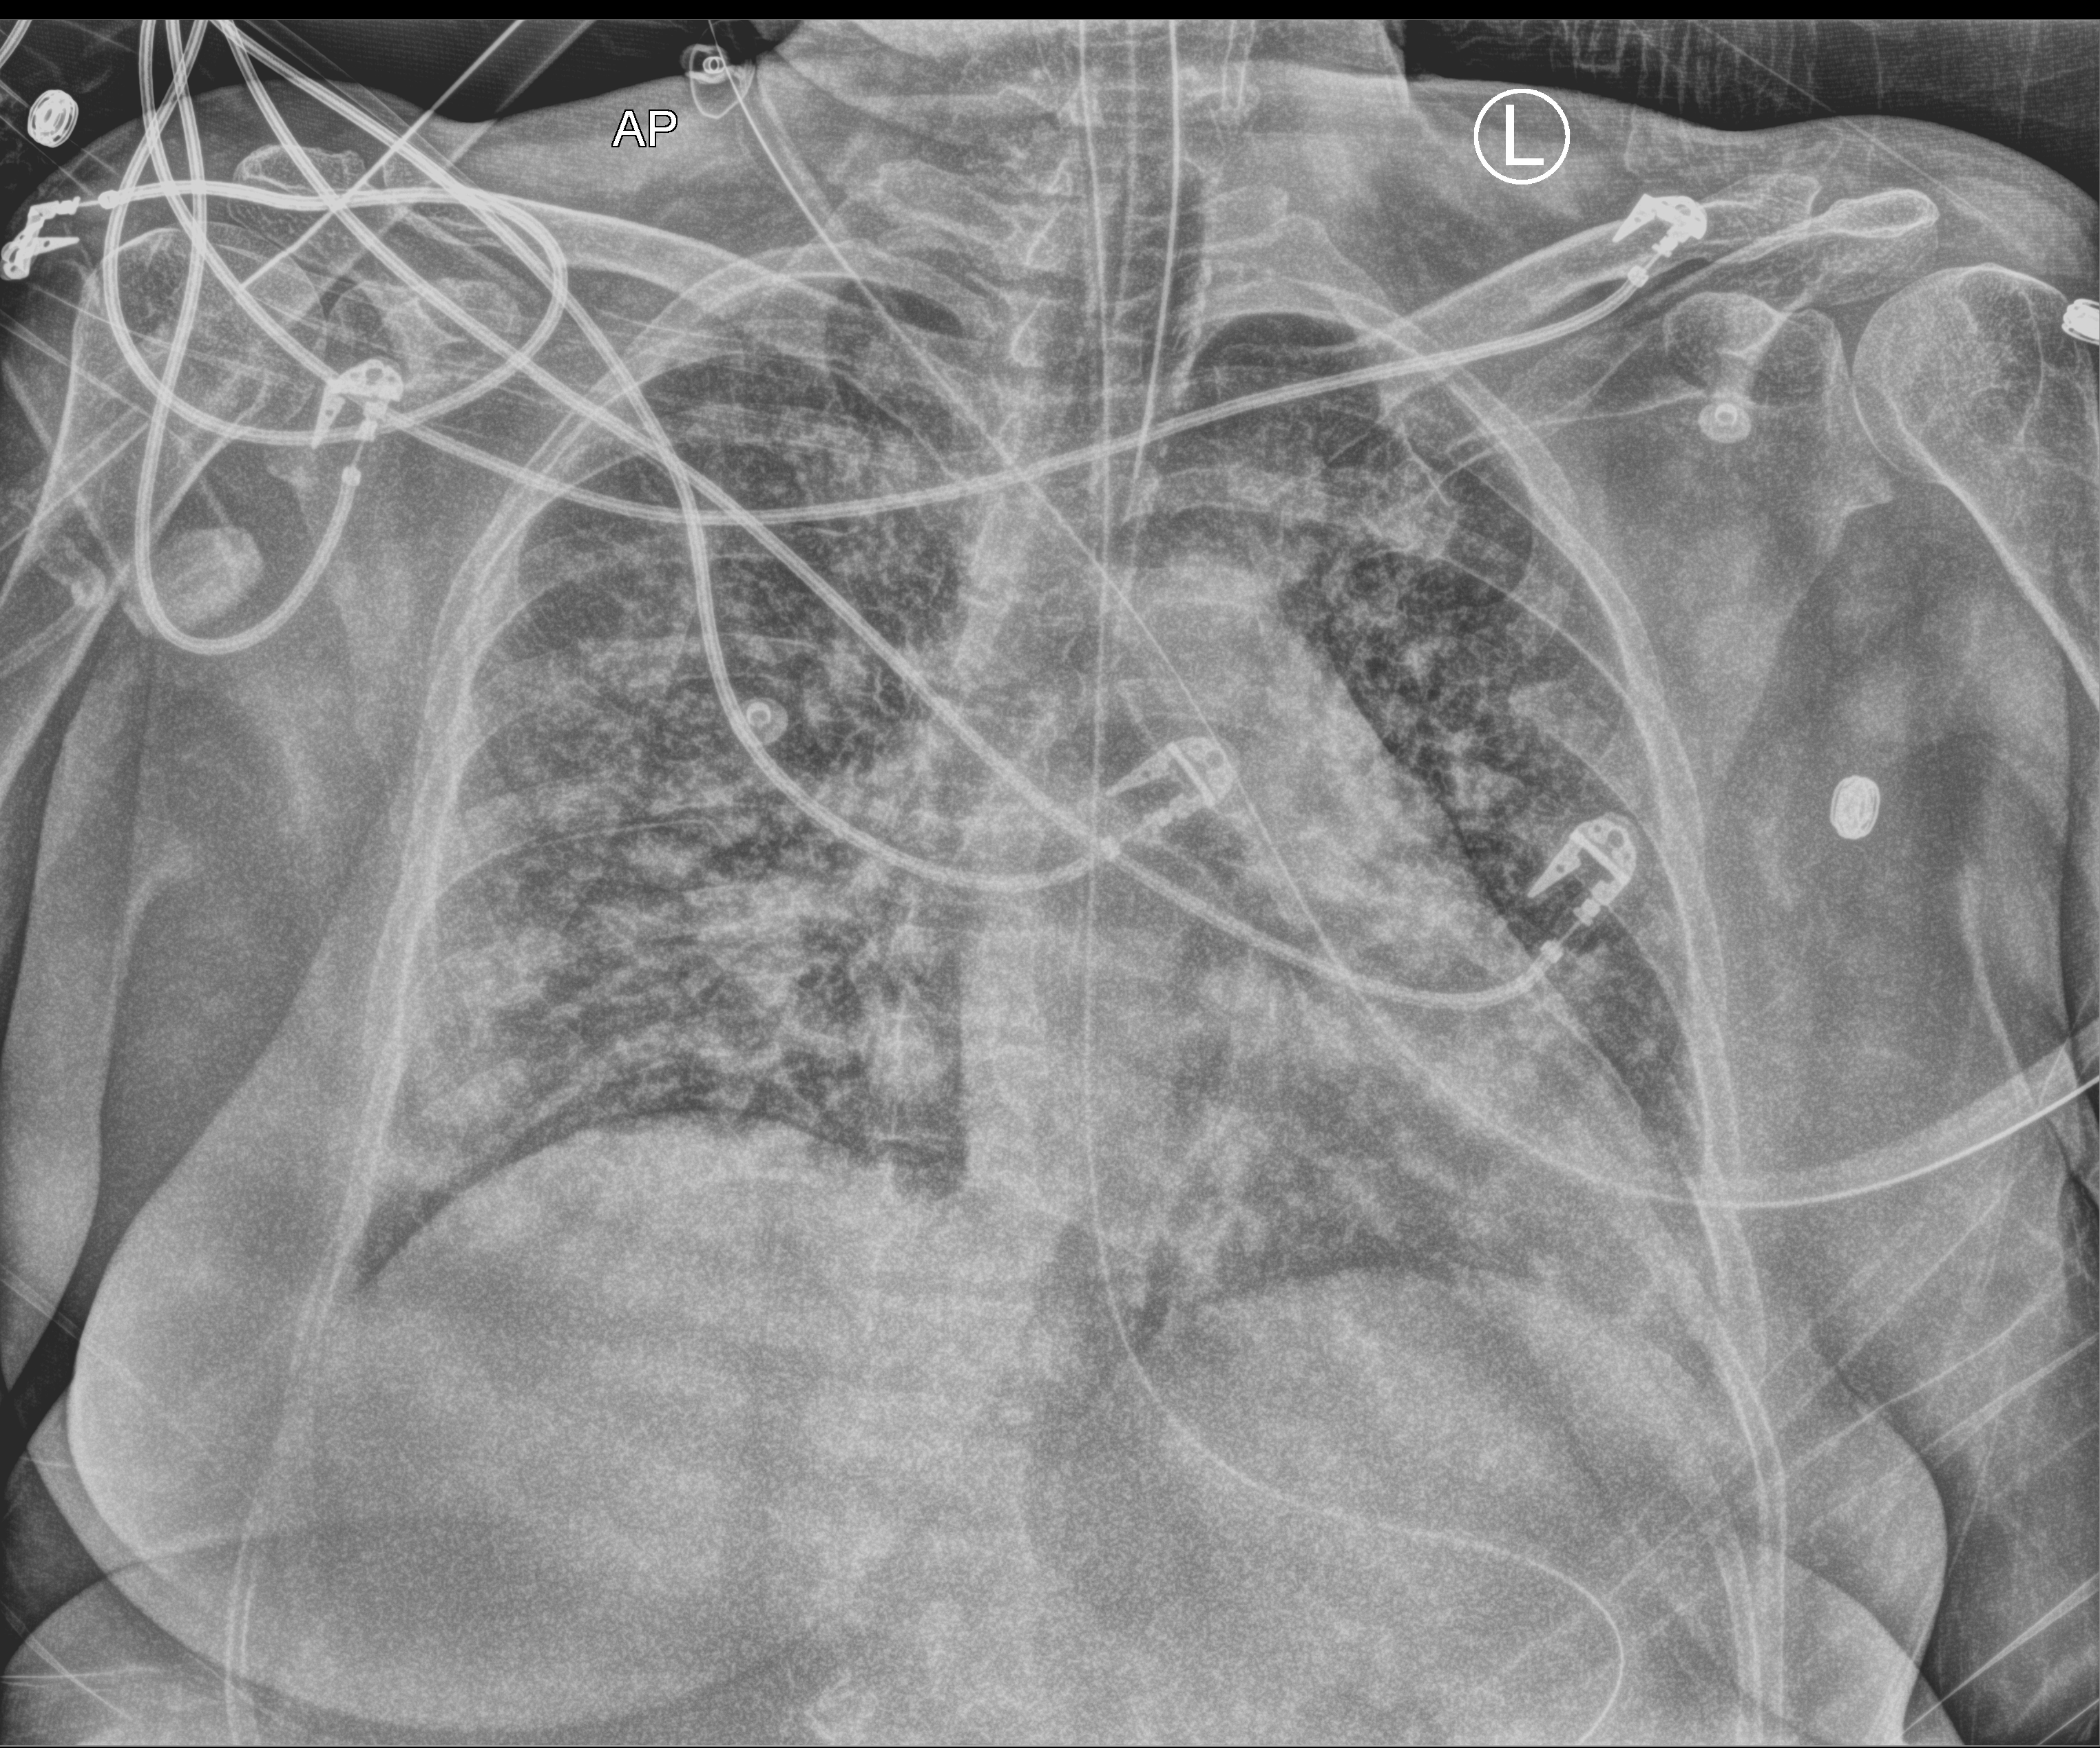
Portable chest radiograph, anteroposterior (AP) projection. Female patient hospitalised with COVID-19, age 18–59 years.
From the hospital-stay record, not from the radiograph (when in the stay this image was taken is not recorded): length of hospital stay: 22 days; hypertension (admission record): no.